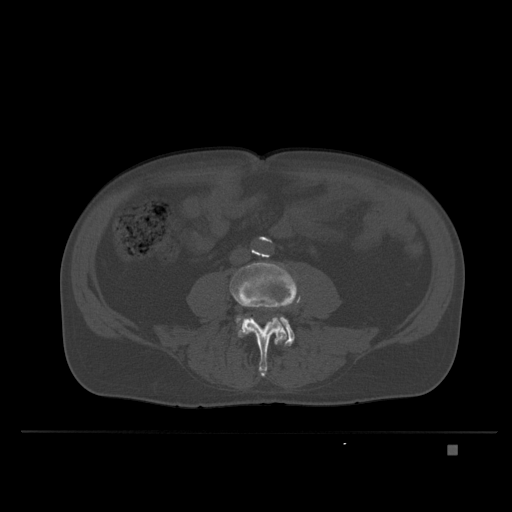
CT including the spine, one axial slice. Slice 71 of 435 in the series (ordered by position). Bone window (W 1800 / L 400 HU). 1.5 mm slice thickness. 512 × 512 image matrix. Patient: male, 73 years. Case-level facts recorded for this patient, not image findings: primary cancer: skin.
Annotated regions visible in this slice (semi-automatically segmented with operator editing):
- L4 vertebra: bounding box (x1, y1, x2, y2) in pixels: (230, 262, 300, 377)
- L5 vertebra: (235, 314, 294, 346)